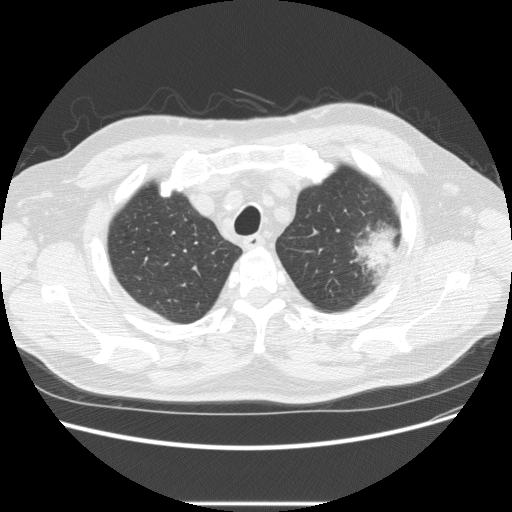
Low-dose screening chest CT, one axial slice. Slice 191 of 233 in the series (ordered by position). Reconstruction kernel STANDARD. 120 kVp. Lung window (W 1500 / L -600 HU). 2.5 mm slice thickness. 512 × 512 image matrix, field of view 380 × 380 mm.
Structures marked on this image (outlined manually by an expert reader):
- lesion 1 (tumor, upper lobe of left lung): box from (x=353, y=225) to (x=401, y=278) px